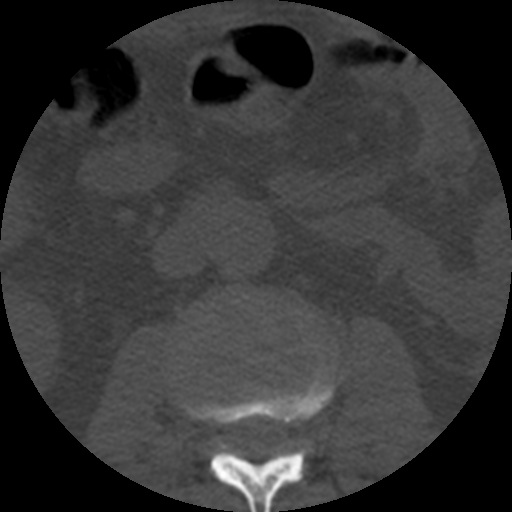
CT including the spine, one axial slice. Position 142 of 508 along the scan axis. Reconstruction kernel STANDARD. Bone window (W 1800 / L 400 HU). 1.25 mm slice thickness. 512 × 512 image matrix, field of view 160 × 160 mm. Patient age 57 years. From the clinical record (not read from this slice): primary cancer: prostate.
Annotated regions visible in this slice (semi-automatically segmented with operator editing):
- L2 vertebra: bounding box (x1, y1, x2, y2) in pixels: (181, 363, 335, 512)